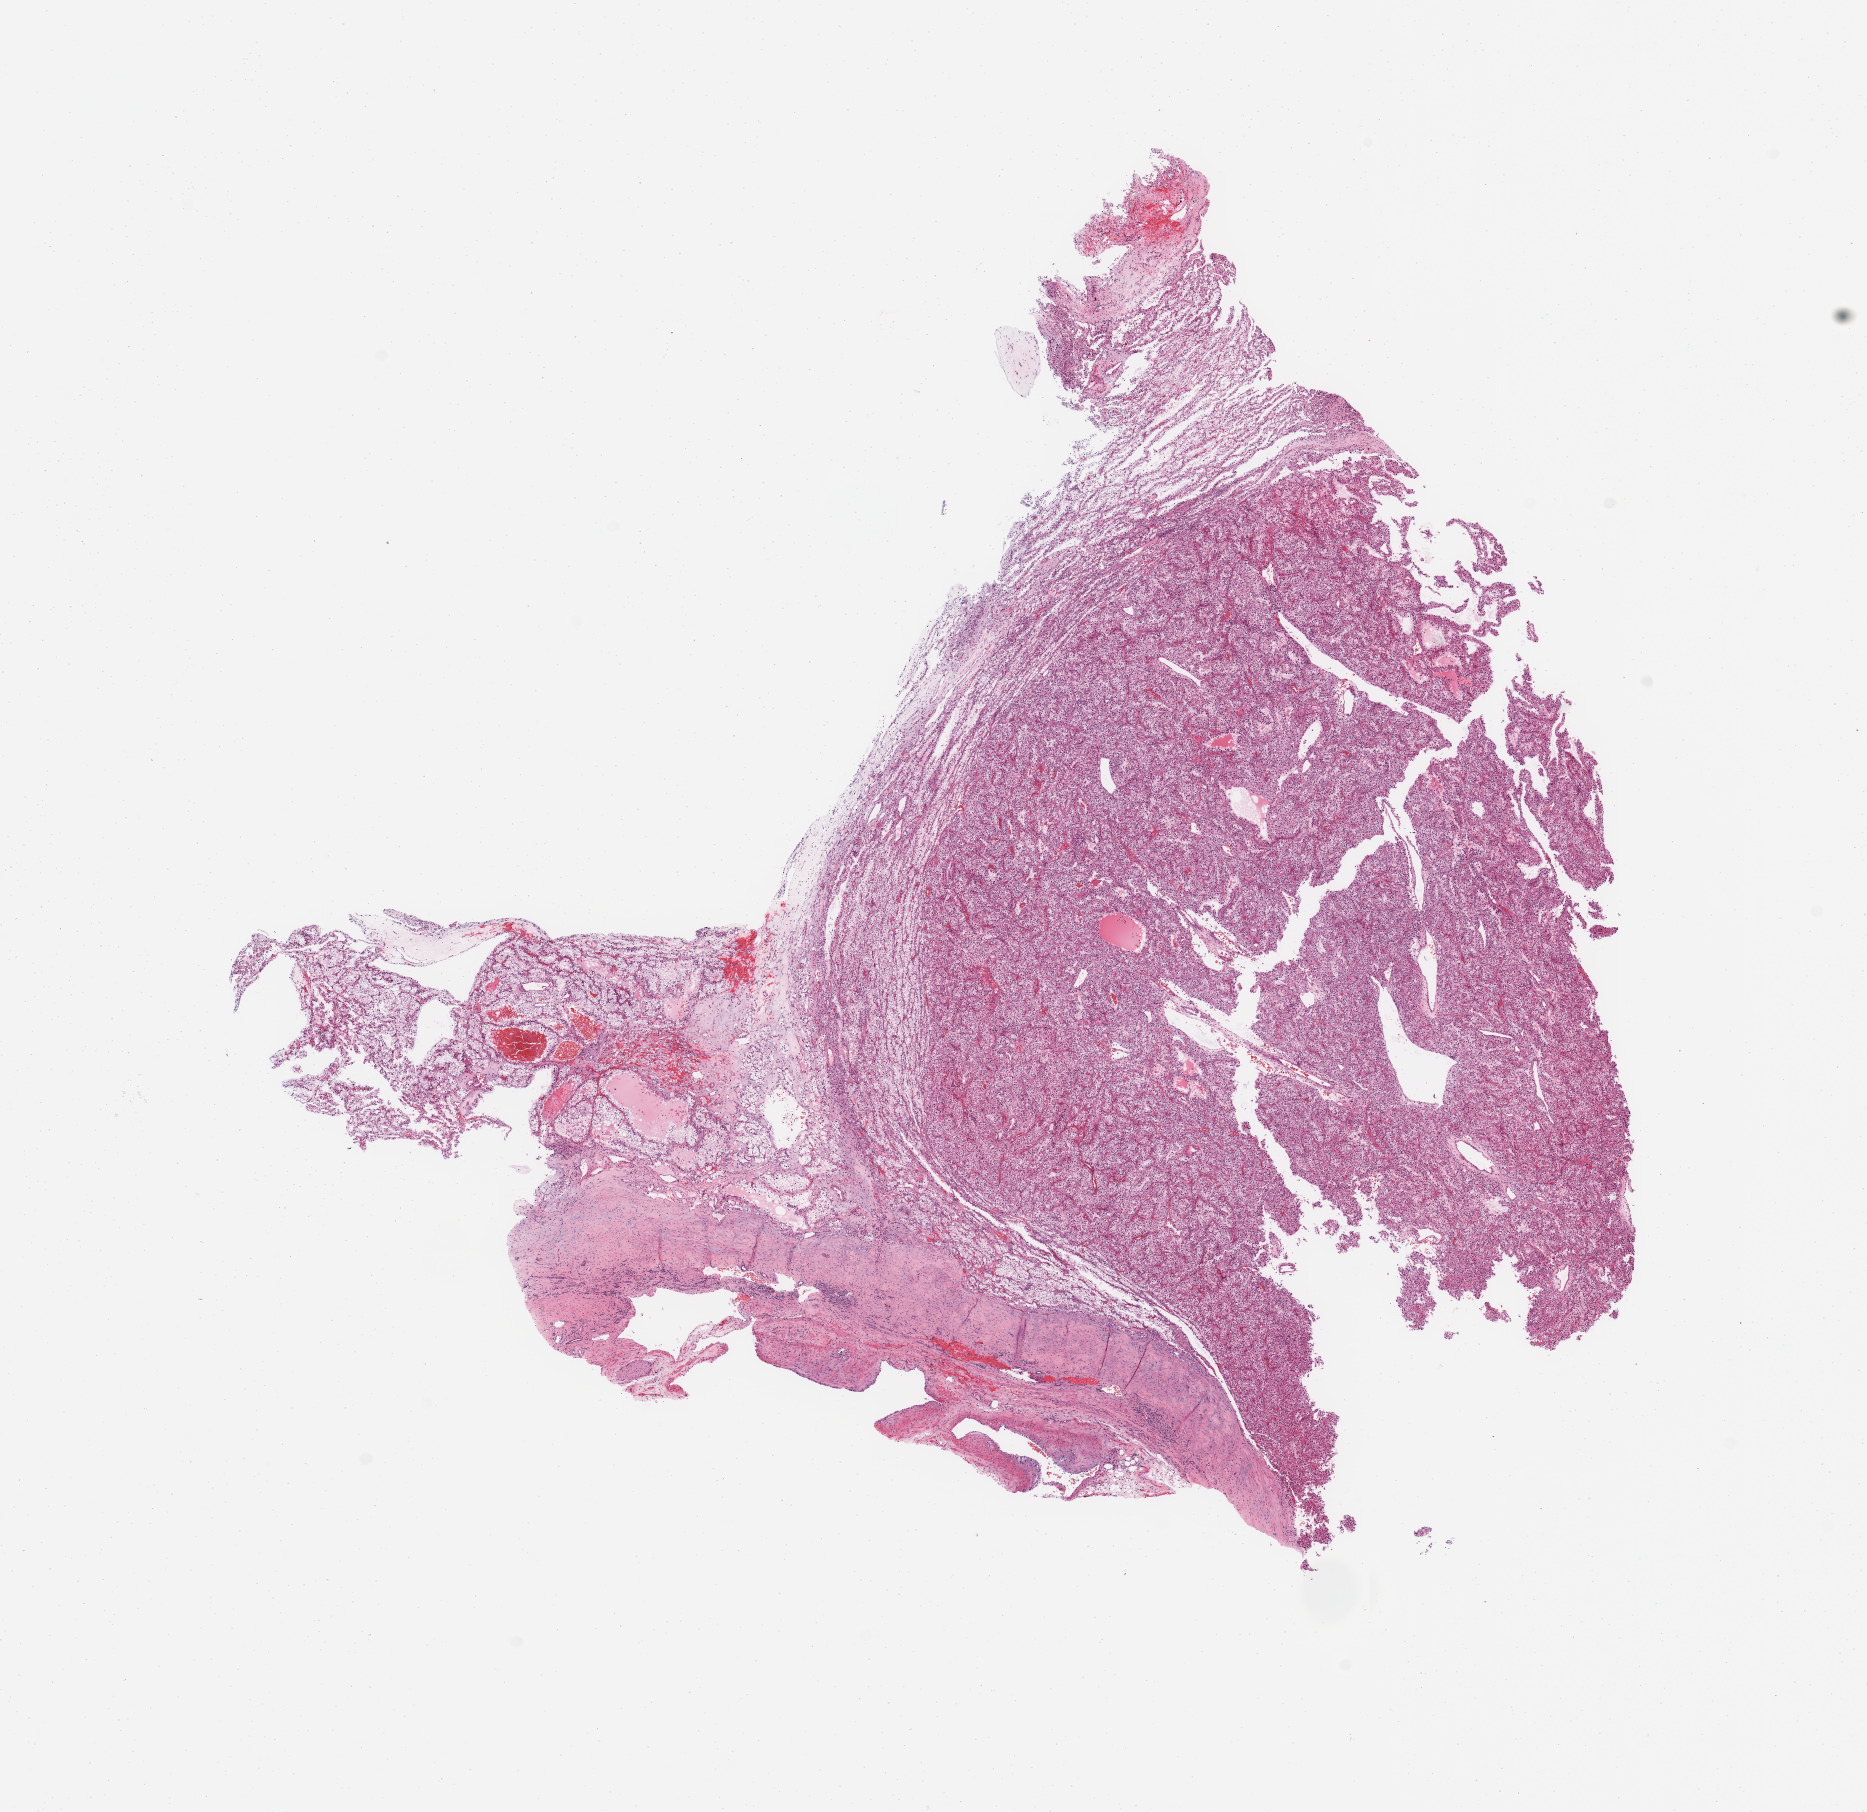
Whole-slide histology image, Hematoxylin and eosin (H&E) stained, whole scanned area (about 14.8 x 14.3 mm, slide scanned at 20x) shown as a low-resolution overview. Tumour tissue sample, sampled site: kidney. Patient: male, age 55 years. Pathologist review of this section (percent, as recorded): tumour nuclei 90%, necrosis 5%.
Diagnosis: Renal cell carcinoma, NOS.